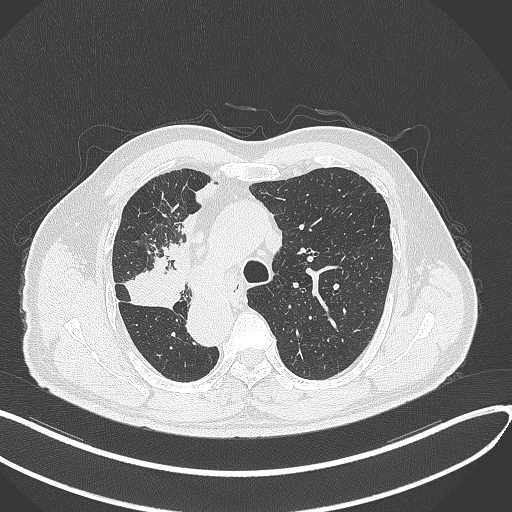
Chest CT, one axial slice. Position 222 of 300 along the scan axis. Reconstruction kernel B70f. 120 kVp. Lung window (W 1500 / L -600 HU). 512 × 512 image matrix, field of view 400 × 400 mm. Male patient, age 67 years. From the clinical record (not read from this slice): clinical TNM (as recorded): T2a N0 M0.
Structures marked on this image (rectangle marked by the reading radiologist):
- lung tumour (recorded histology: squamous cell carcinoma): bounding box <122,252,189,313> (left, top, right, bottom; pixels)